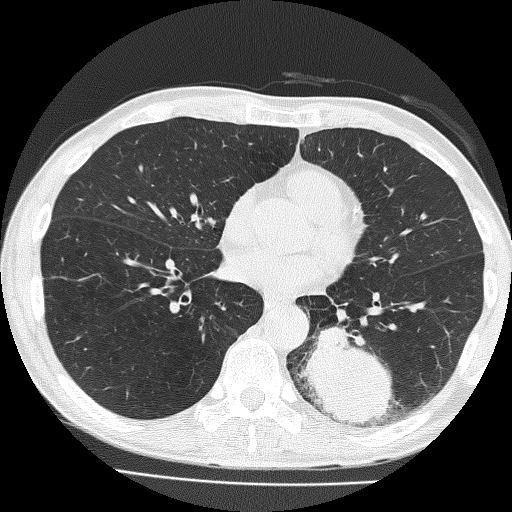
Low-dose screening chest CT, one axial slice. Position 73 of 160 along the scan axis. Reconstruction kernel FC51. 120 kVp. Lung window (W 1500 / L -600 HU). 2 mm slice thickness. 512 × 512 image matrix.
Structures marked on this image (manually delineated by an expert):
- lesion 1 (tumor, lower lobe of left lung): bounding box (x1, y1, x2, y2) in pixels: (302, 326, 393, 424)